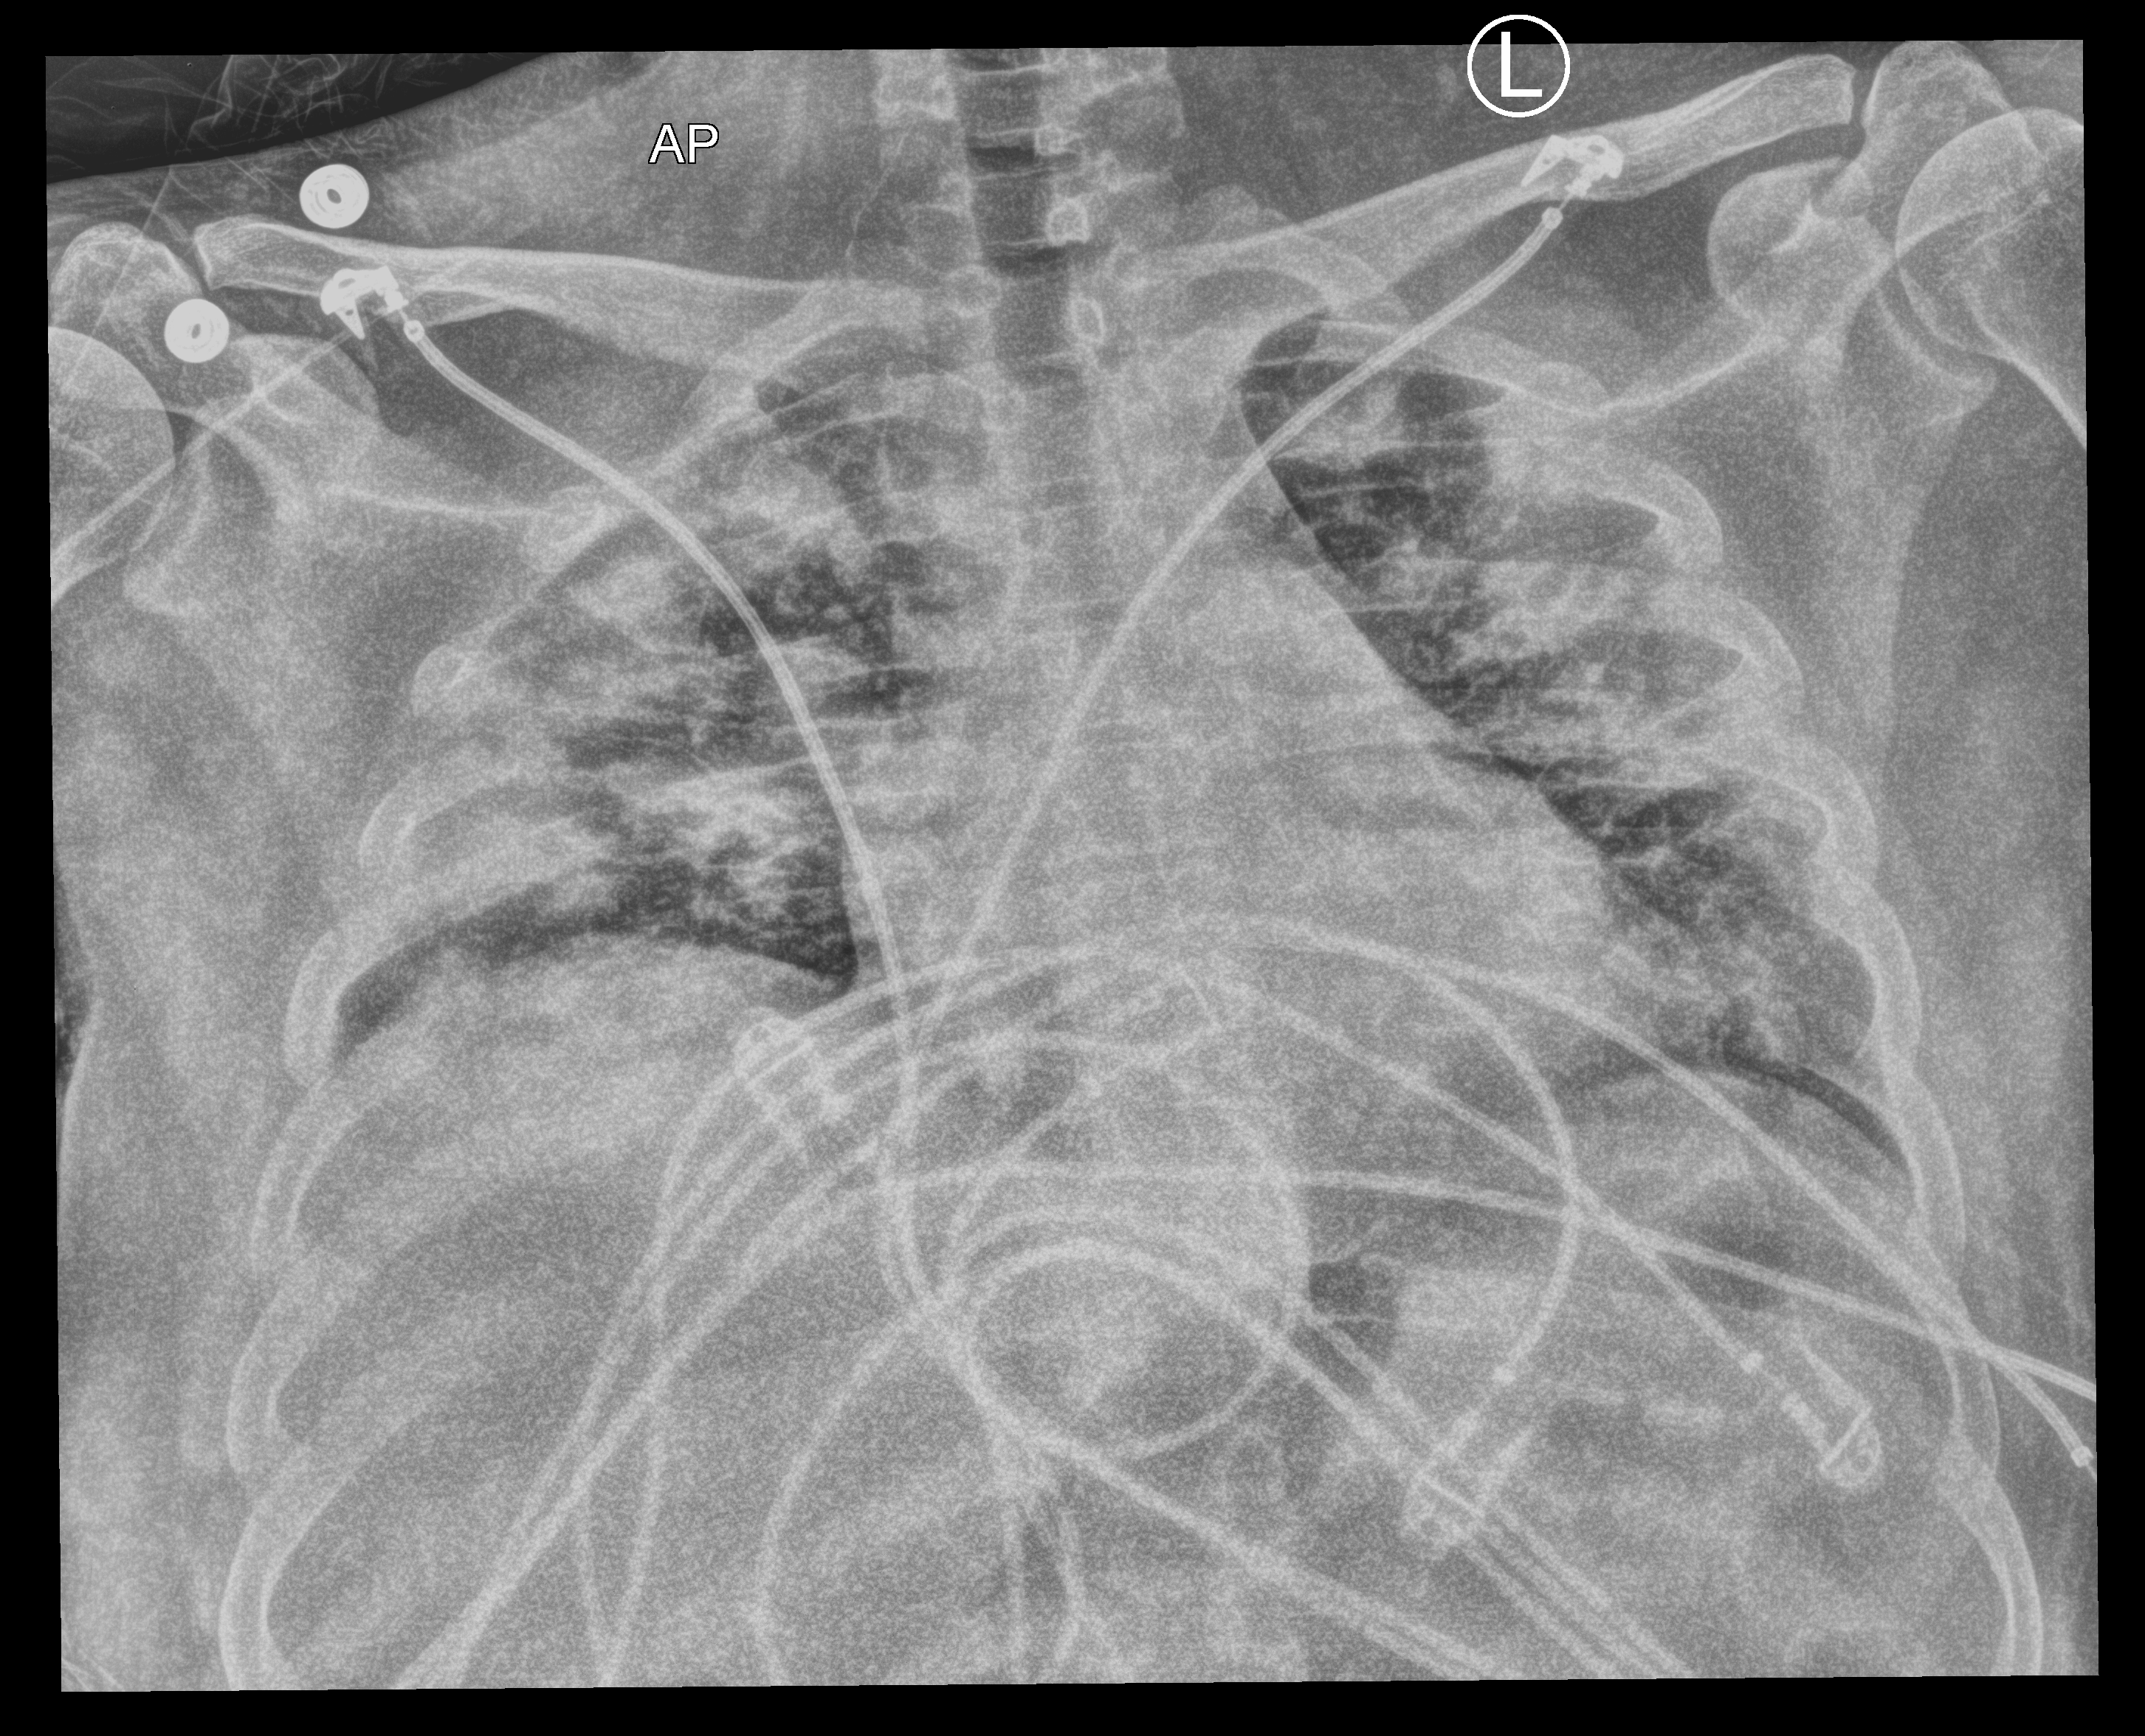
Bedside chest radiograph (computed radiography). Patient hospitalised with COVID-19; male, aged 18–59 years.
Hospital-stay facts (about this admission, not read from this image; timing relative to this image not recorded):
- length of hospital stay: 44 days
- admitted to intensive care during this hospital stay: yes